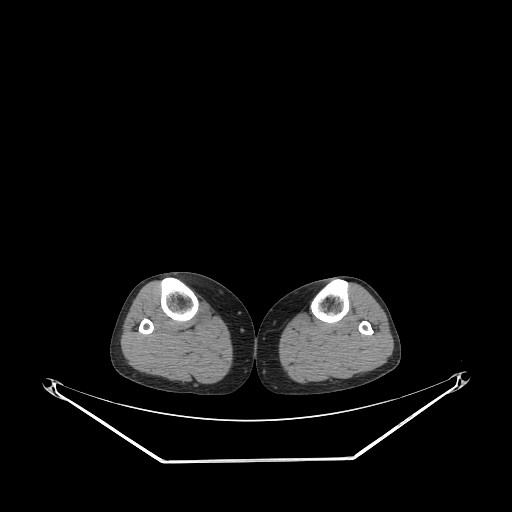
CT of an extremity soft-tissue mass (from a PET/CT study), one axial slice; position 154 of 267 along the scan axis; reconstruction kernel STANDARD; 140 kVp; soft-tissue window (W 400 / L 40 HU); 3.75 mm slice thickness; 512 × 512 image matrix, field of view 500 × 500 mm. Female patient. Case-level facts recorded for this patient, not image findings: histological type: undifferentiated – high grade; grade: high; site of the primary tumour: right thigh.
Outlined on this slice (expert contour drawn on MRI and transferred to this co-registered scan by the dataset authors):
- gross tumour volume (mass): box from (x=196, y=301) to (x=213, y=325) px